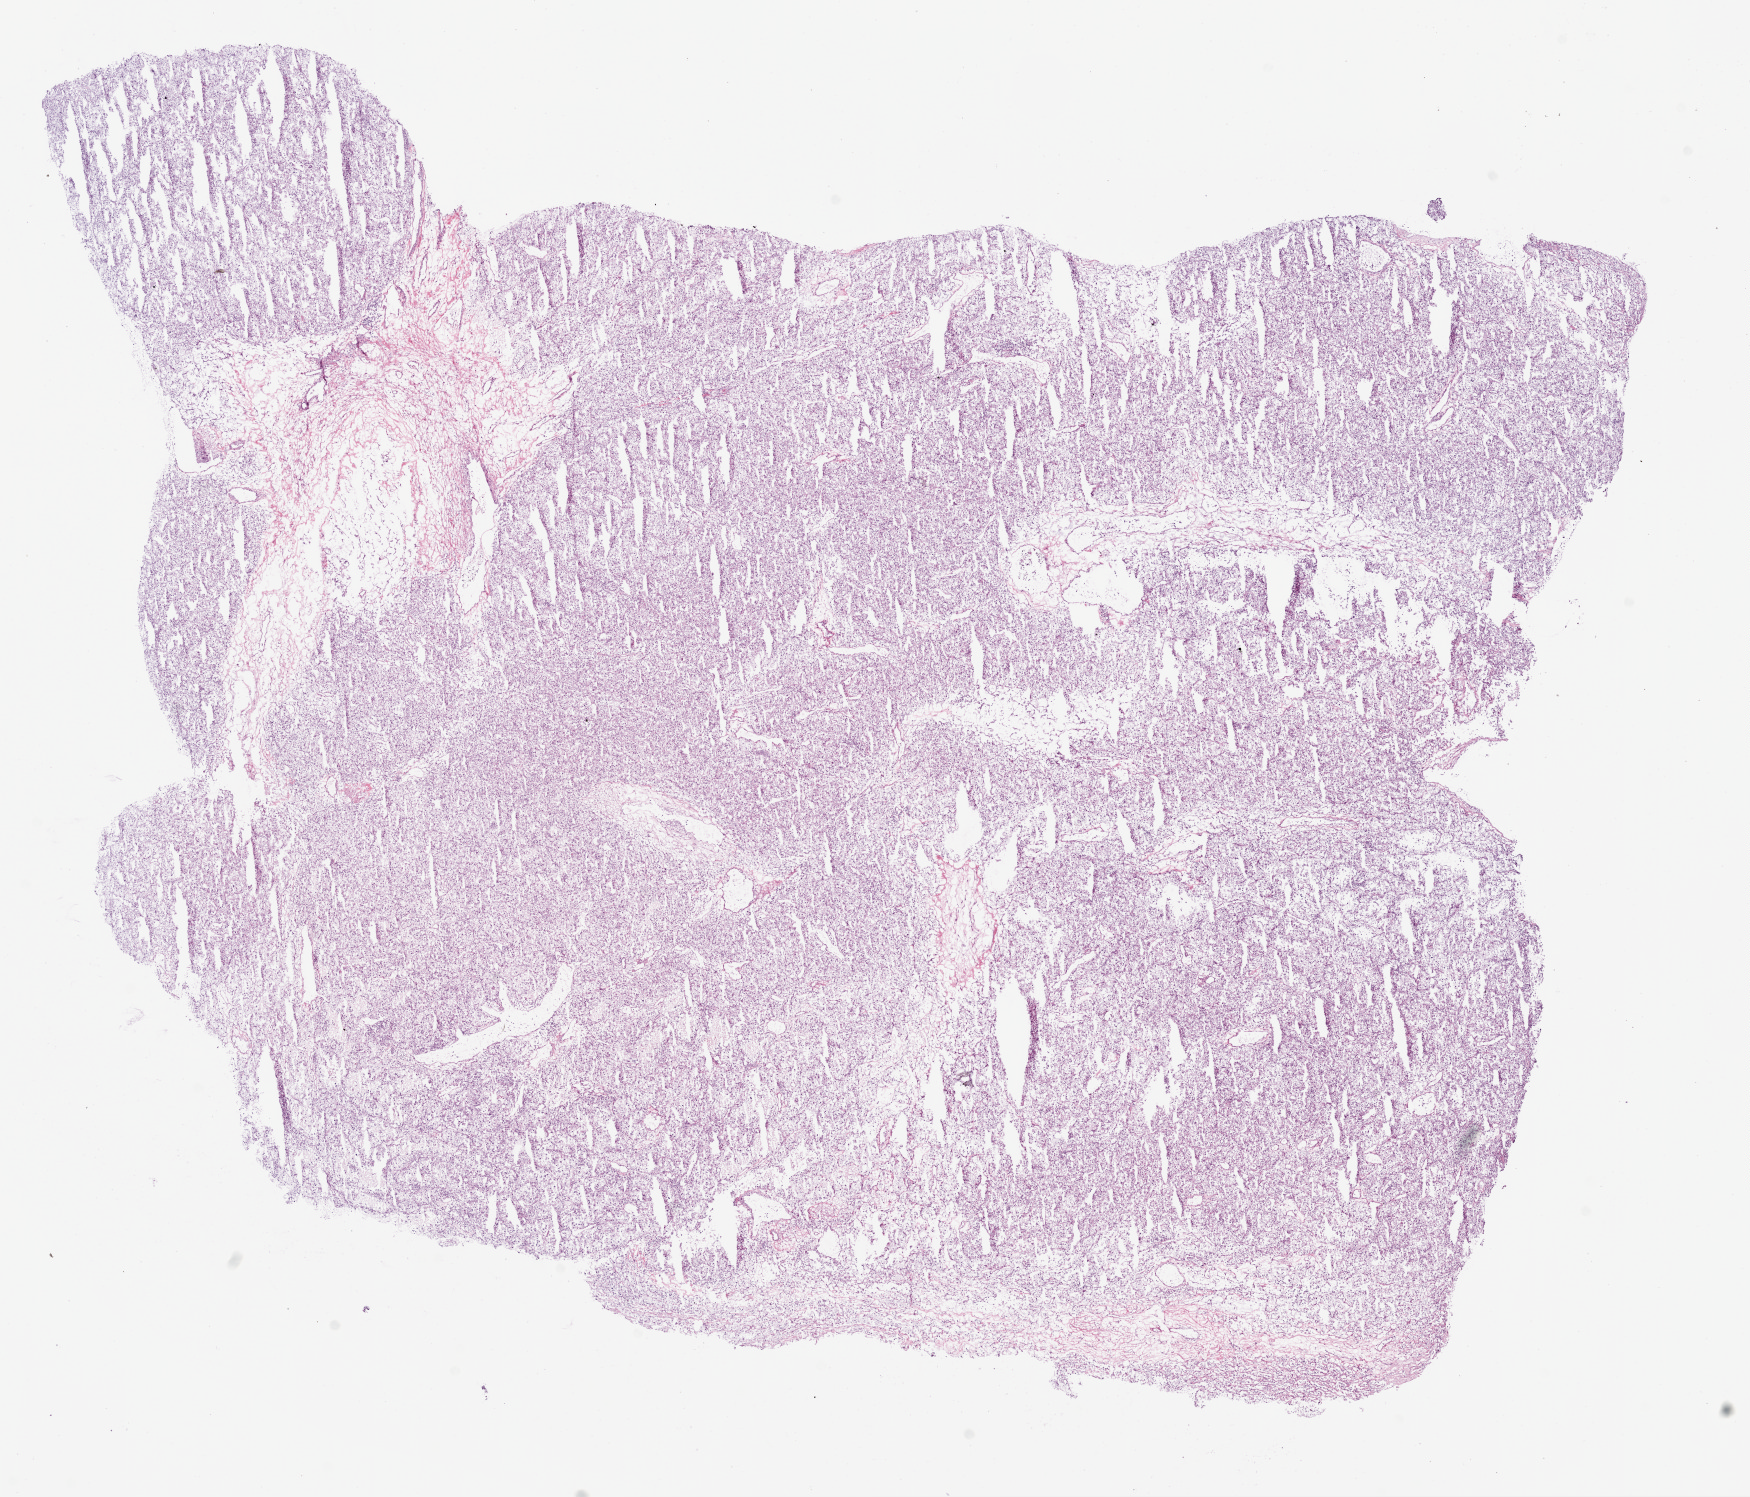
H&E whole-slide image — a low-resolution overview of the entire scanned area, about 14.0 x 12.0 mm (from a 20x scan); frozen section from the bottom of the tissue portion; kidney, primary tumour sample. Patient: male, age at initial diagnosis 63 years. Histologic grade: G3 (poorly differentiated). Composition of this section per pathologist review: tumour cells 90%, tumour nuclei 85%, normal cells 0%, stromal cells 10%, necrosis 0%.
Diagnosis: Clear cell adenocarcinoma, NOS. AJCC pathologic stage: I.